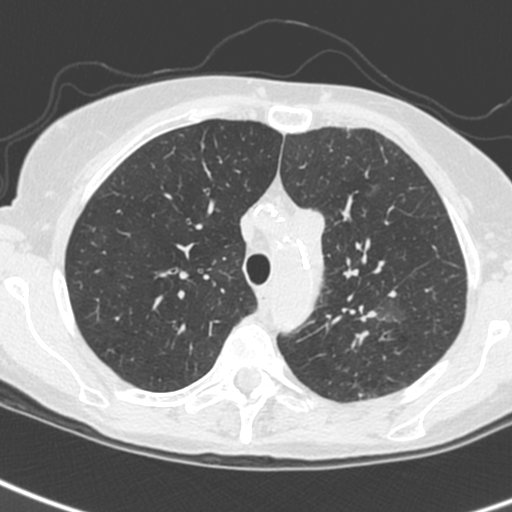
Low-dose screening chest CT, one axial slice; slice 188 of 242 in the series (ordered by position); lung window (W 1500 / L -600 HU); 1.3 mm slice thickness; 512 × 512 image matrix, field of view 284 × 284 mm.
Annotated regions visible in this slice (manually delineated by an expert):
- lesion 3 (tumor, upper lobe of left lung): bounding box (x1, y1, x2, y2) in pixels: (296, 208, 325, 297)